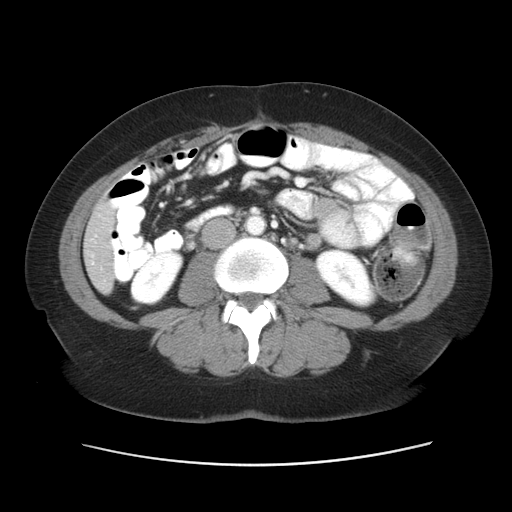
Contrast-enhanced abdominal CT, one axial slice. Position 14 of 52 along the scan axis. Reconstruction kernel STANDARD. Intravenous contrast given. Soft-tissue window (W 400 / L 40 HU). 5 mm slice thickness. 512 × 512 image matrix. Female patient, age 48 years. From the clinical record (not read from this slice): diagnosis: colorectal cancer liver metastases, imaged before liver resection; multiple liver metastases: yes.
Outlined on this slice (outlined manually by an expert reader):
- liver: box from (x=86, y=202) to (x=114, y=290) px